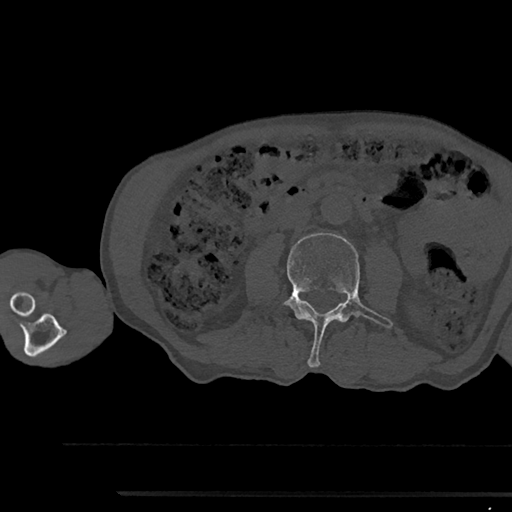
CT including the spine, one axial slice; slice 489 of 797 in the series (ordered by position); reconstruction kernel Br40s/3; bone window (W 1800 / L 400 HU); 512 × 512 image matrix. Male patient, age 79 years. Case-level facts recorded for this patient, not image findings: primary cancer: prostate.
Outlined on this slice (semi-automatically segmented with operator editing):
- L3 vertebra: bounding box <284,233,393,367> (left, top, right, bottom; pixels)